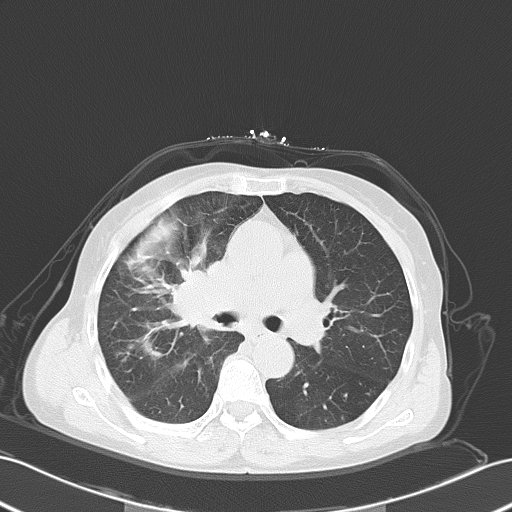
Chest CT, one axial slice; slice 33 of 55 in the series (ordered by position); reconstruction kernel B70f; 120 kVp; lung window (W 1500 / L -600 HU); 512 × 512 image matrix, field of view 353 × 353 mm. Female patient, age 67 years. Case-level facts recorded for this patient, not image findings: clinical TNM (as recorded): T2a N3 M0; histopathological grade: G3.
Structures marked on this image (rectangle marked by the reading radiologist):
- lung tumour (recorded histology: small cell carcinoma): bounding box <169,262,235,330> (left, top, right, bottom; pixels)